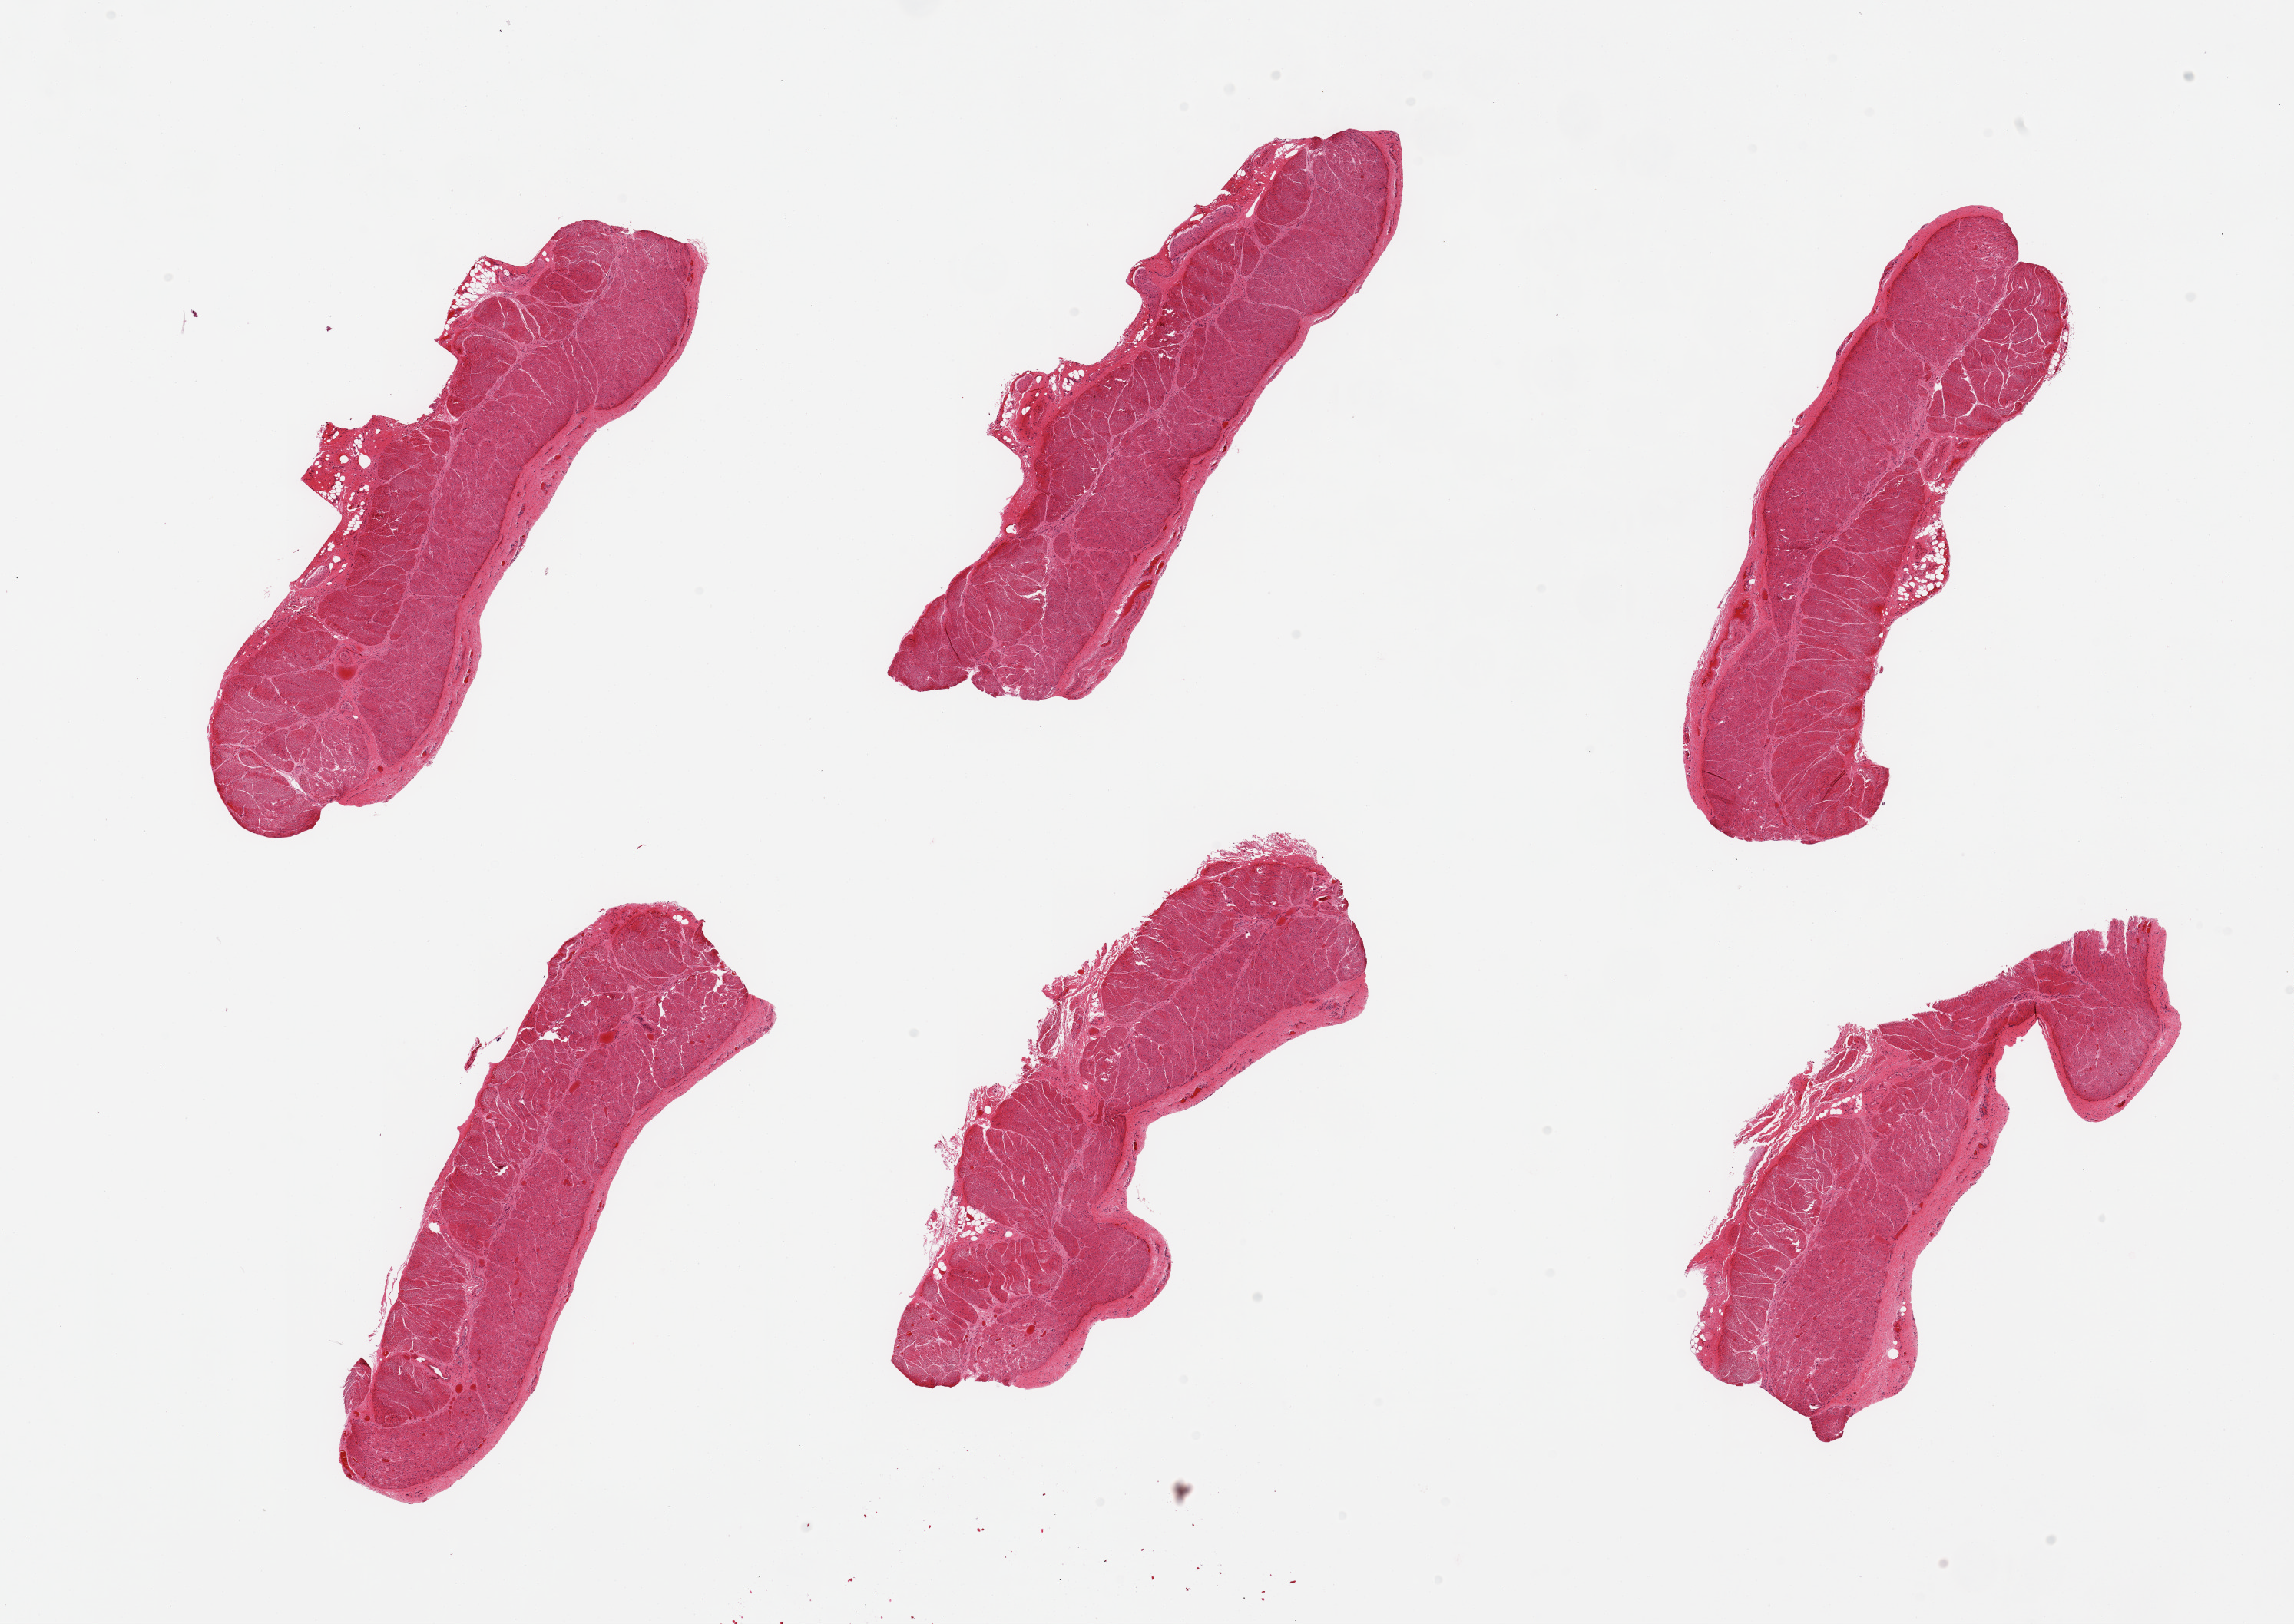
Hematoxylin and eosin (H&E) whole-slide image — a low-resolution overview of the entire scanned area, about 23.6 x 16.7 mm. PAXgene-fixed, paraffin-embedded tissue. Sampled site (target tissue): esophageal muscle. Donor tissue sample. Donor: male.
Reviewer comment on this tissue sample: 6 pieces; well trimmed muscularis.